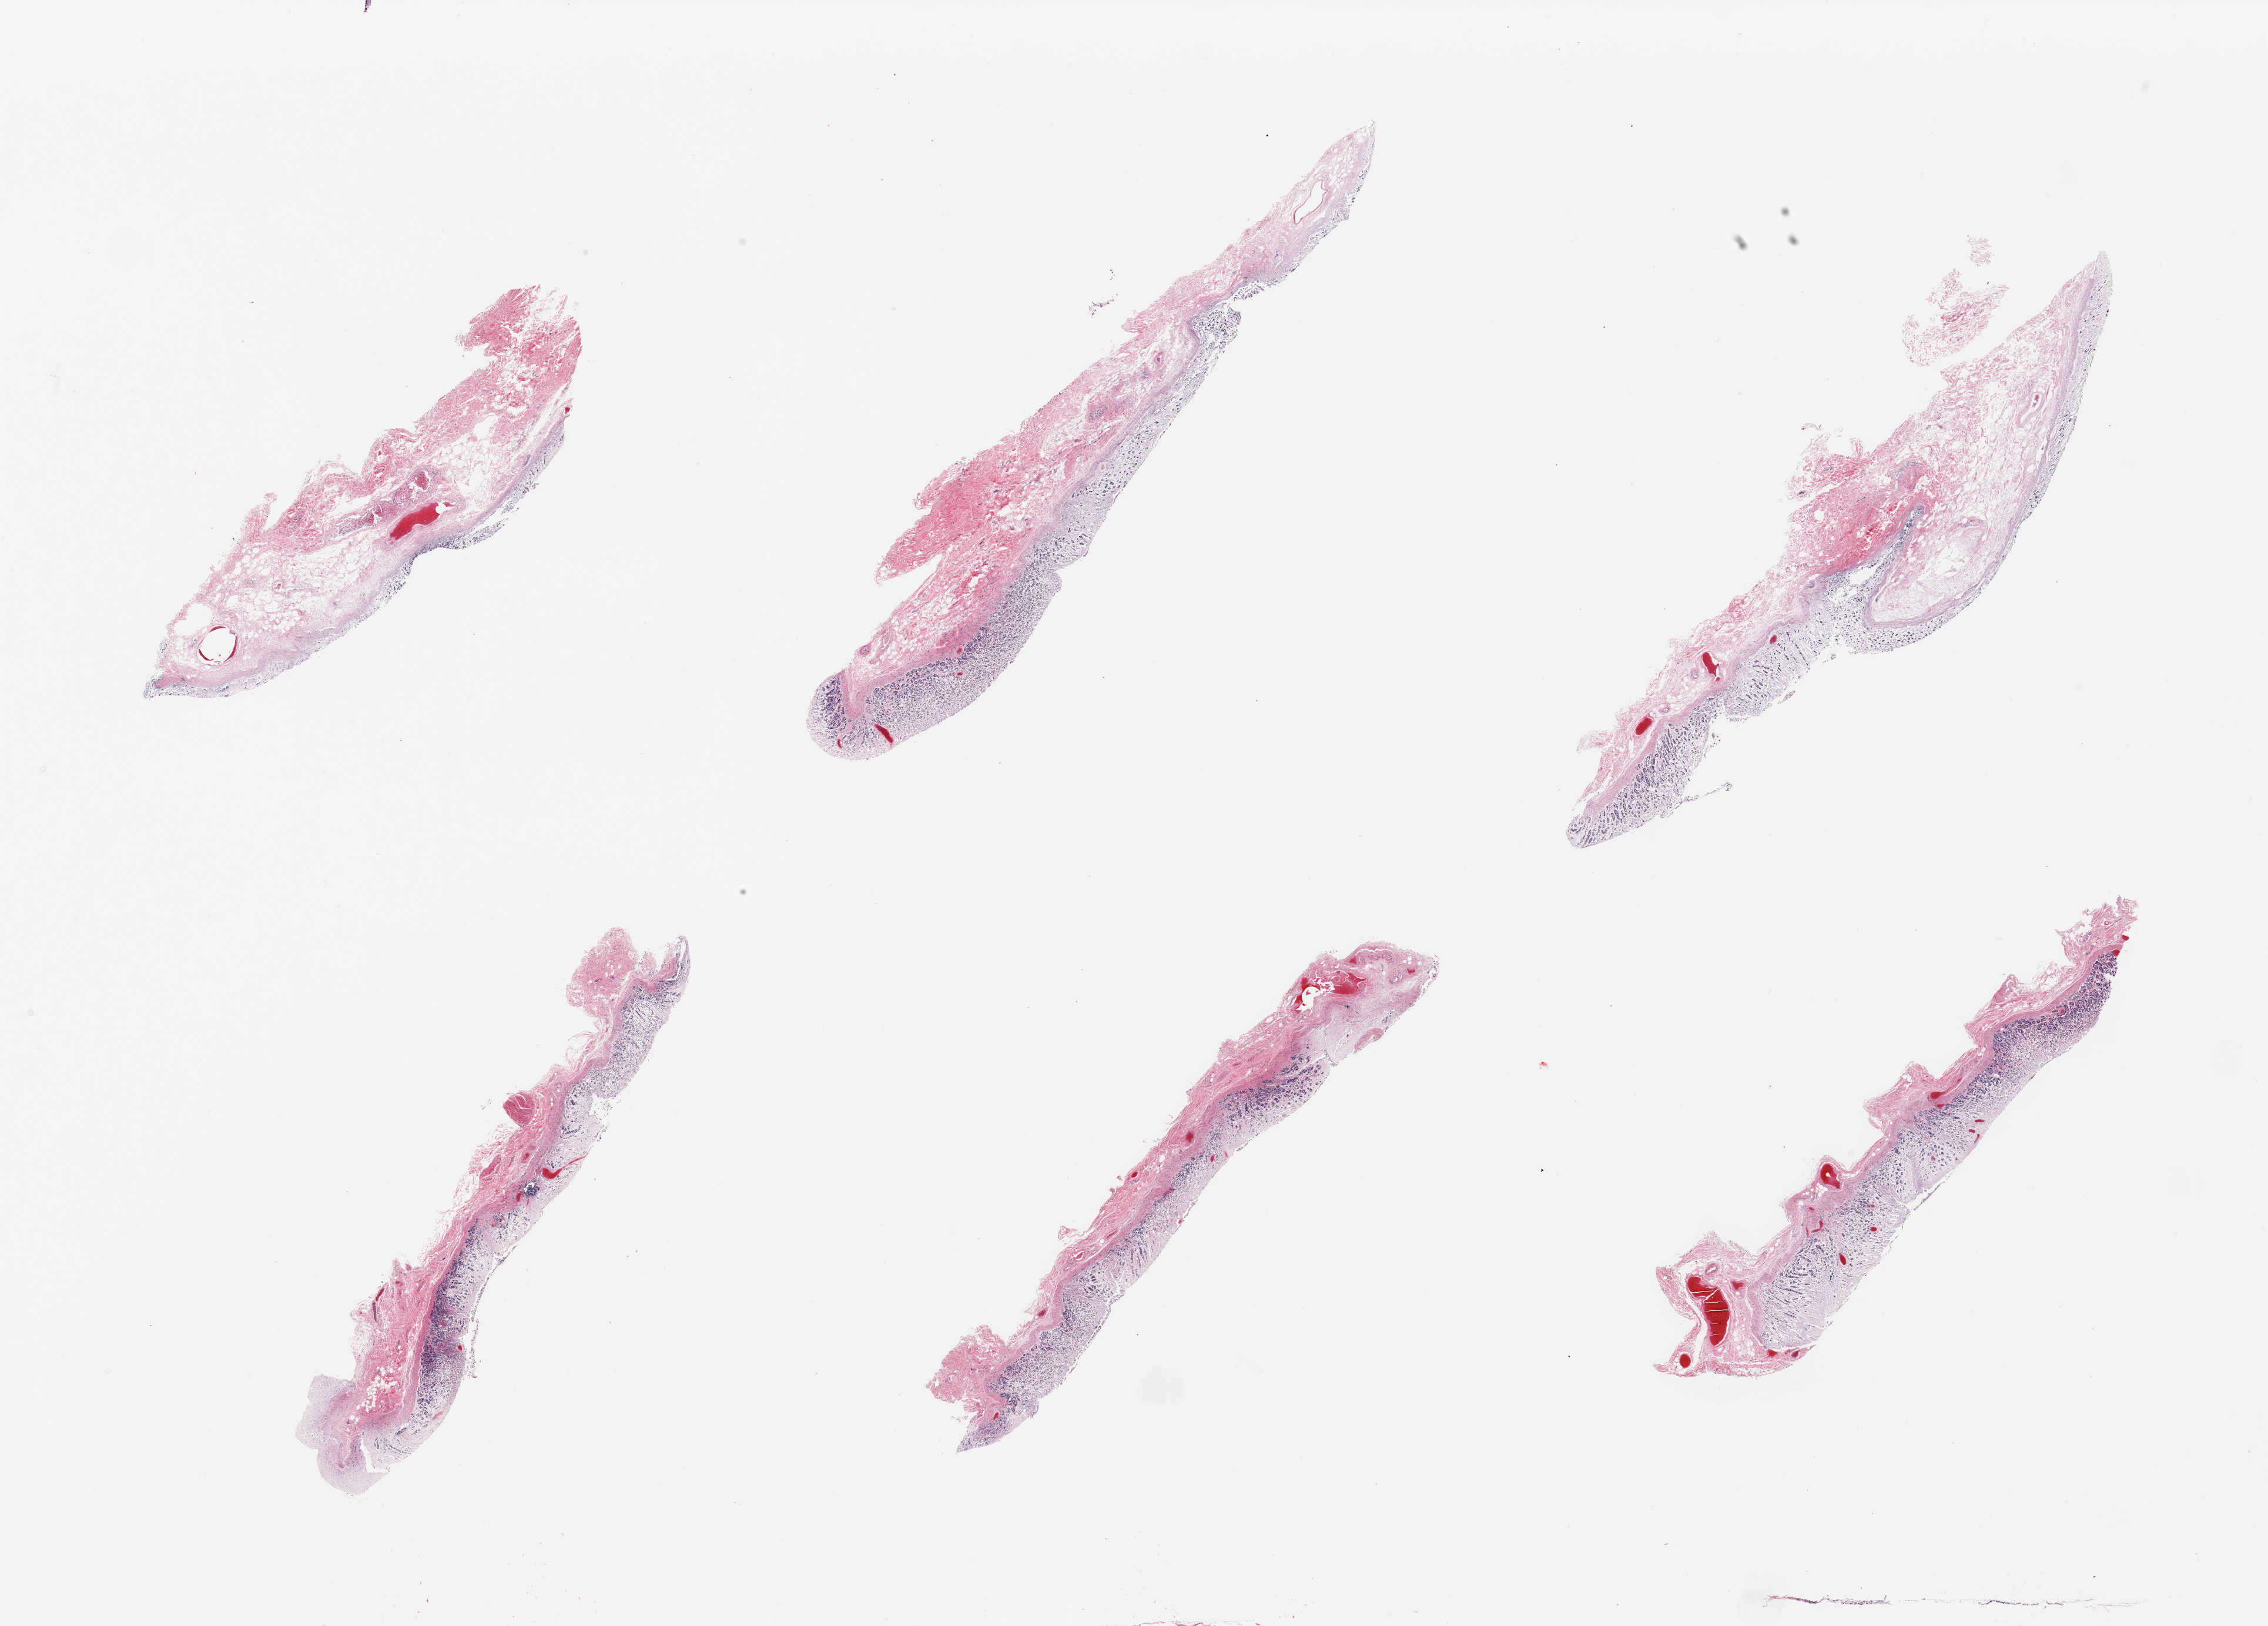
Hematoxylin and eosin (H&E) whole-slide image, brightfield — low-resolution overview of the scanned area, about 30.5 x 21.9 mm. PAXgene-fixed, paraffin-embedded tissue. Target tissue: stomach. Donor tissue sample.
Review note (as recorded): 6 pieces, mucosa completely autolyzed.